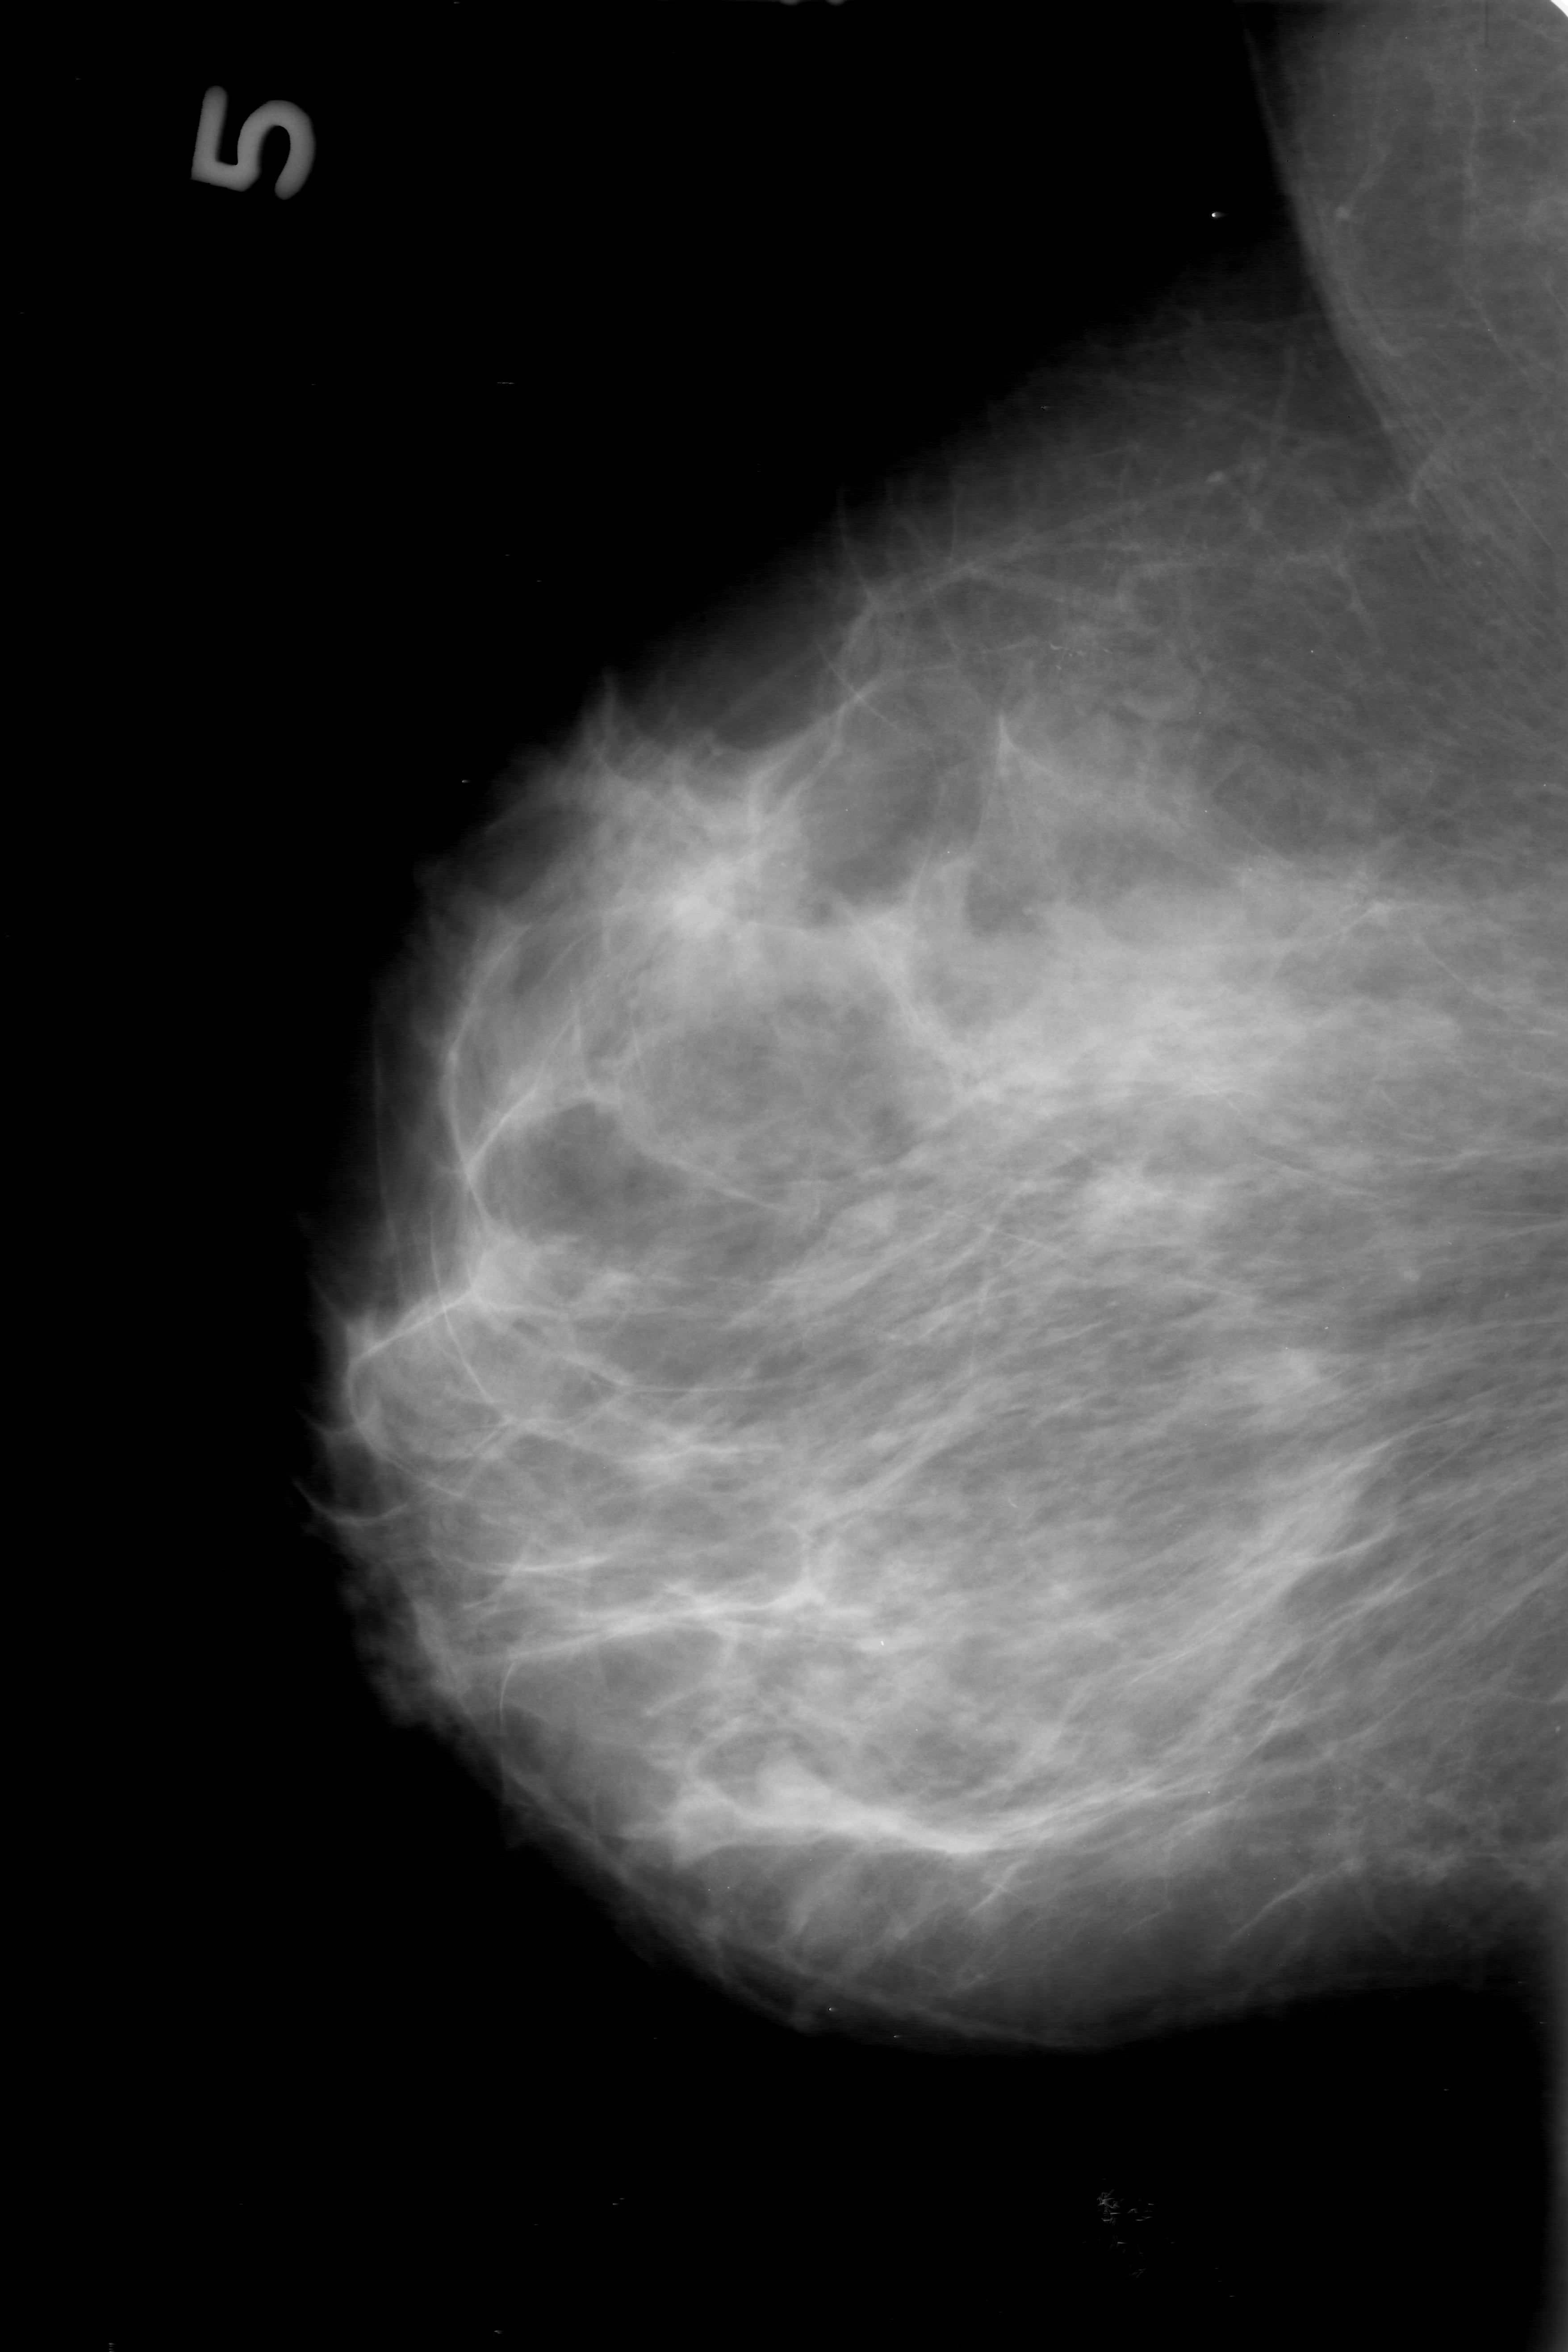
Digitized screen-film mammogram; right breast; mediolateral oblique (MLO) view; breast composition: heterogeneously dense (BI-RADS density category 3 of 4); 1568 × 2352 image matrix.
Expert-marked regions of interest on this image (one box per marked abnormality):
- calcifications, morphology punctate / amorphous, distribution clustered; BI-RADS assessment category 0 (incomplete: needs additional imaging); pathology (as recorded): benign: bounding box [x1, y1, x2, y2] px = [1182, 797, 1356, 959]